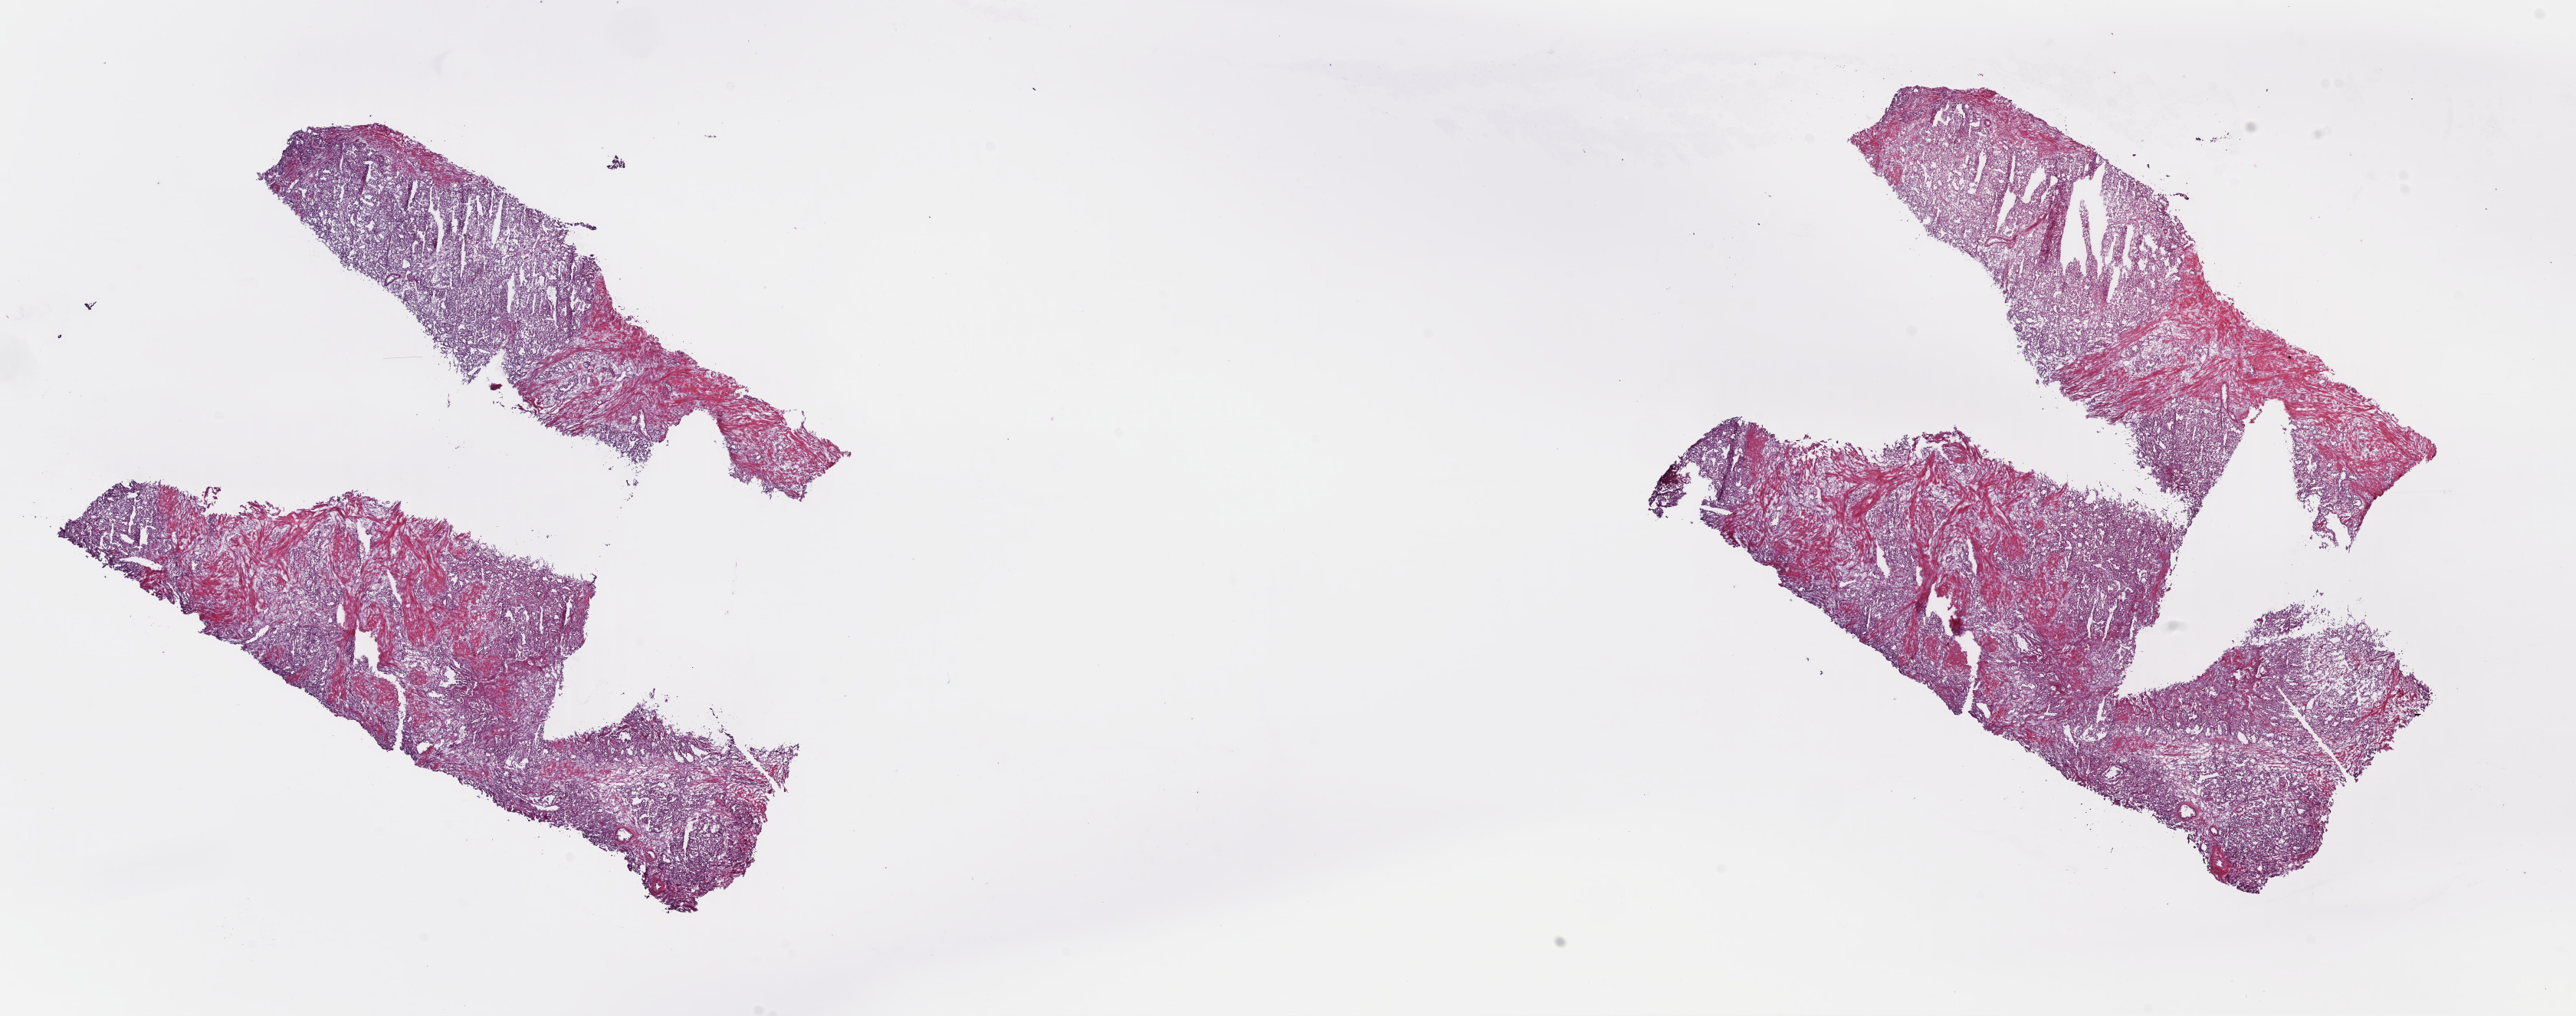
Digitized H&E-stained tissue section (whole slide), shown as a low-resolution overview of the whole scanned area (about 26.4 x 10.4 mm), frozen section from the top of the tissue portion, sample: primary tumour, kidney. Patient: male, age at initial diagnosis 53 years. Histologic grade: G2 (moderately differentiated). Slide review estimates, as recorded: tumour cells 65%, tumour nuclei 80%, normal cells 0%, stromal cells 35%, necrosis 0%. Infiltration values recorded for this section: lymphocyte infiltration 0%, monocyte infiltration 0%, neutrophil infiltration 0%.
Histologic diagnosis: Clear cell adenocarcinoma, NOS. AJCC pathologic stage: I (6th edition).